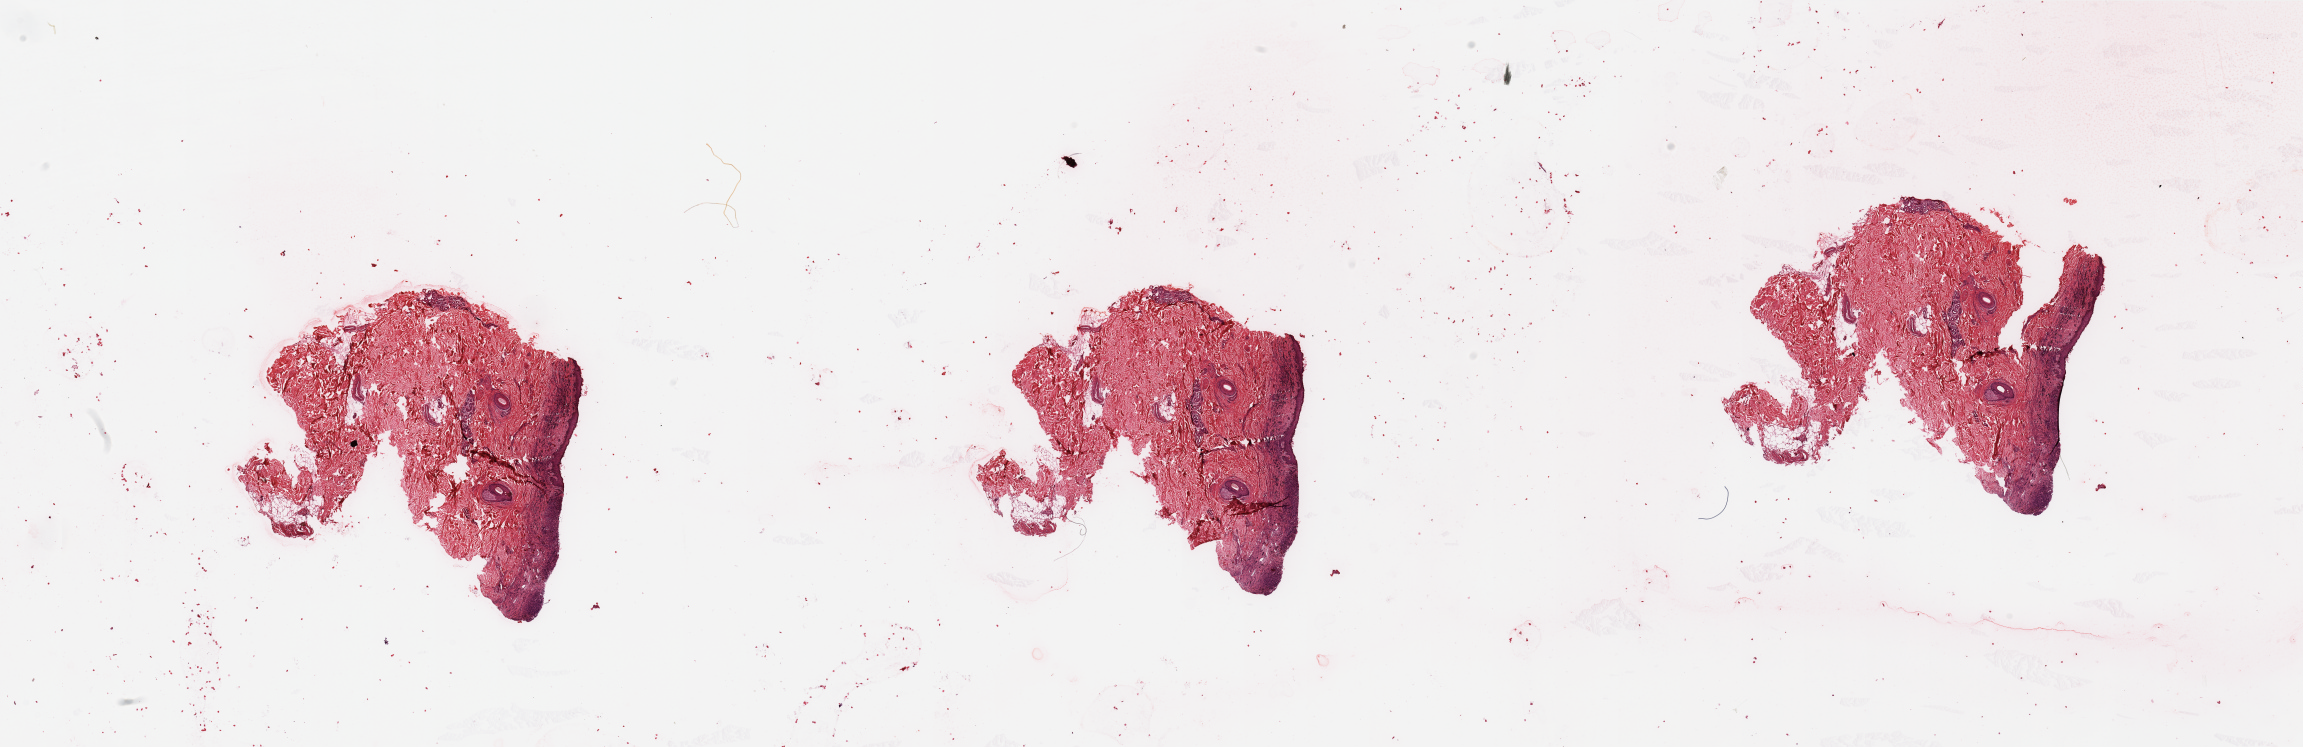
Hematoxylin and eosin (H&E) stained whole-slide image — whole scanned area (about 36.4 x 11.8 mm, from a 20x scan) shown as a low-resolution overview. Melanoma tumour tissue; sampled site not recorded. Male, 69 y/o.
Histologic diagnosis: Malignant melanoma, NOS. Primary tumour site (as recorded): trunk. AJCC pathologic stage: IIA.